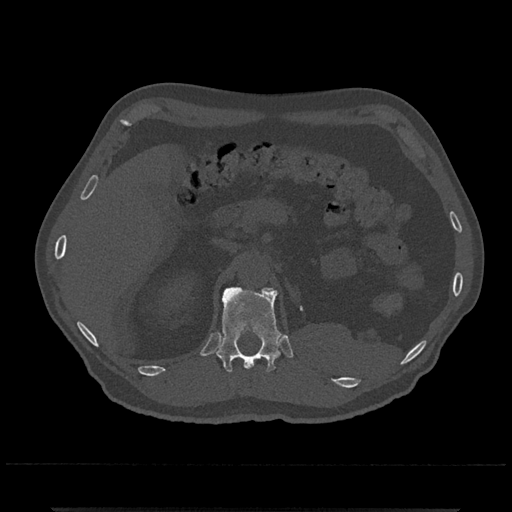
CT including the spine, one axial slice; slice 433 of 797 in the series (ordered by position); reconstruction kernel Br40s/3; 120 kVp; bone window (W 1800 / L 400 HU); 512 × 512 image matrix. Male patient, age 67 years. From the clinical record (not read from this slice): primary cancer: prostate.
Outlined on this slice (semi-automatically segmented with operator editing):
- T12 vertebra: bounding box (x1, y1, x2, y2) in pixels: (216, 286, 281, 372)